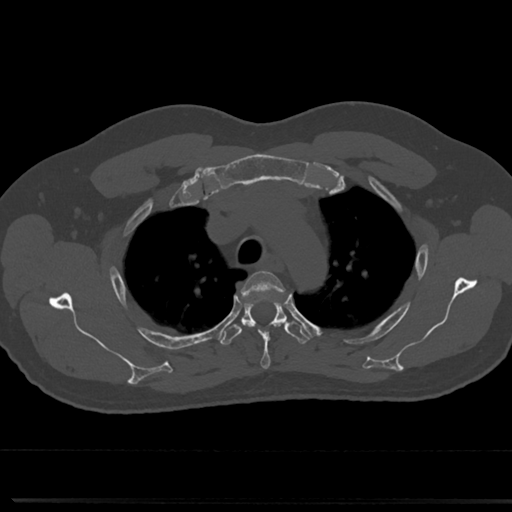
CT including the spine, one axial slice; slice 567 of 817 in the series (ordered by position); reconstruction kernel Br40s/3; bone window (W 1800 / L 400 HU); 0.5 mm slice thickness; 512 × 512 image matrix. Male patient, age 61 years. Case-level facts recorded for this patient, not image findings: primary cancer: prostate.
Outlined on this slice (semi-automatic segmentation, software-assisted and operator-edited):
- T3 vertebra: bounding box (x1, y1, x2, y2) in pixels: (242, 270, 283, 369)
- T4 vertebra: (219, 299, 310, 346)